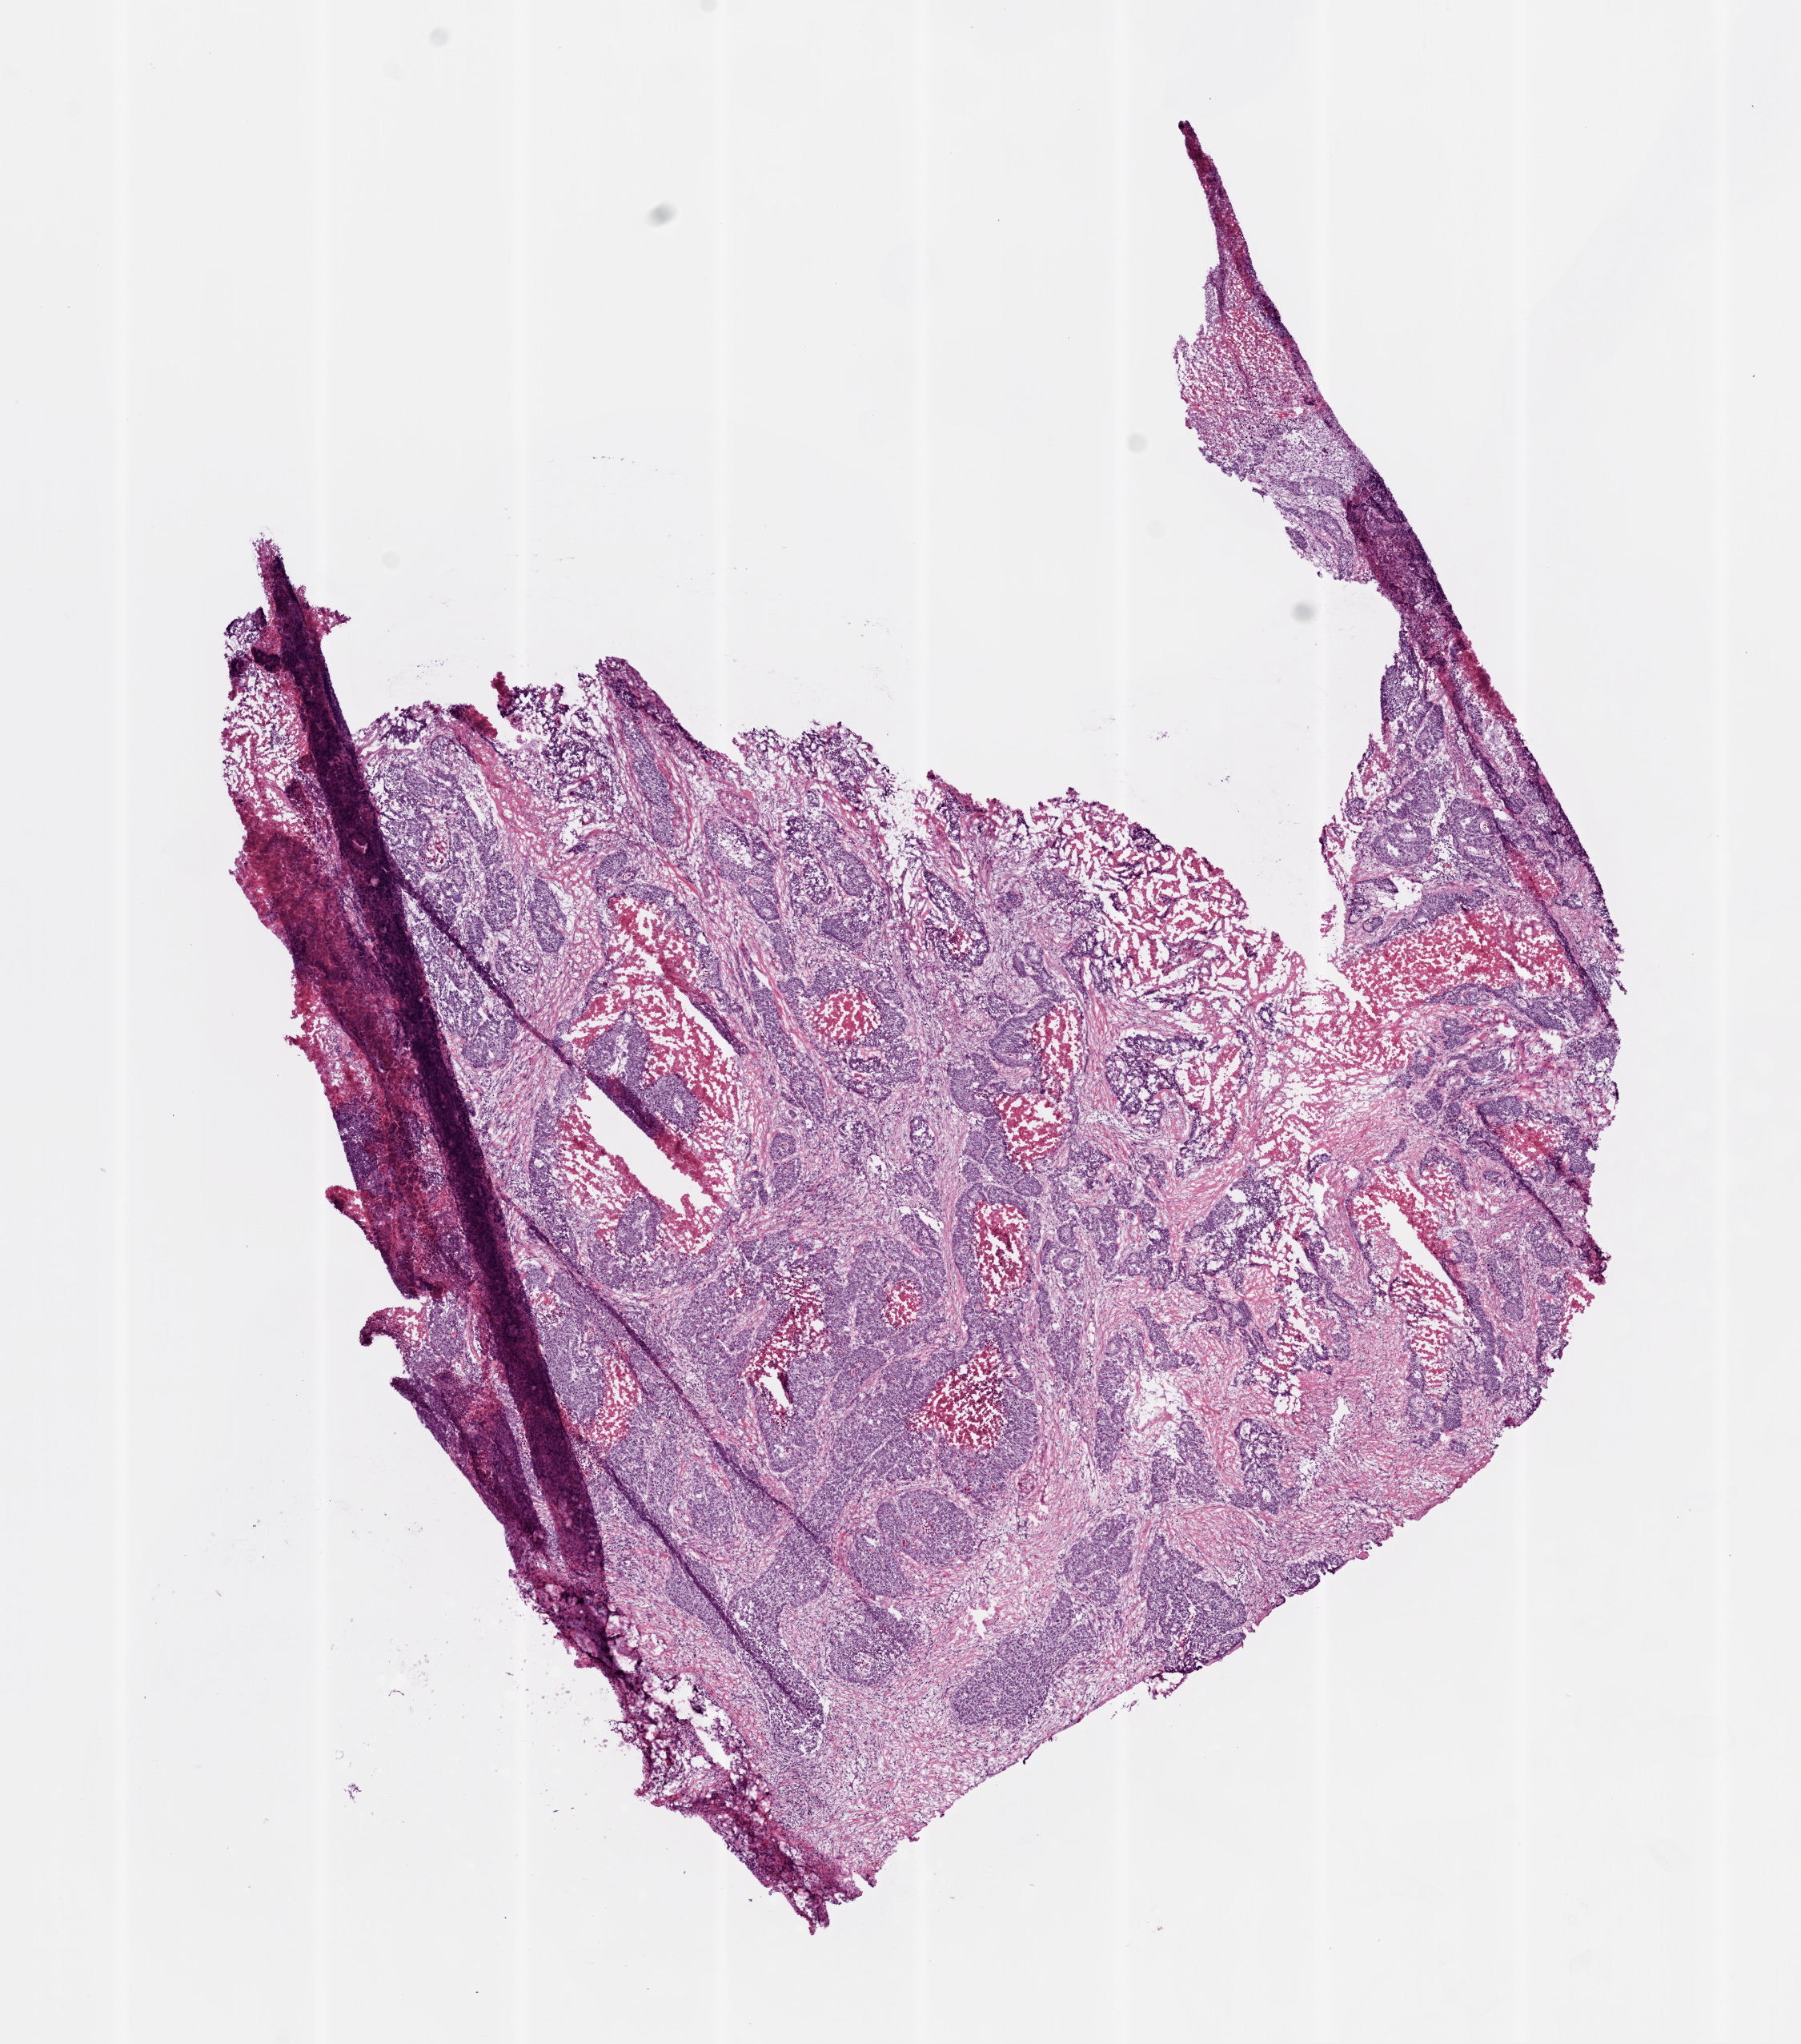
Digitized H&E tissue section (whole slide) — low-resolution overview of the scanned area, about 9.0 x 10.2 mm; frozen section; stomach, primary tumour sample. Patient: male, age at initial diagnosis 66 years. Histologic grade: G3 (poorly differentiated). Slide review estimates, as recorded: tumour cells 62%, tumour nuclei 80%, normal cells 0%, stromal cells 20%, necrosis 18%.
Pathologic diagnosis: Adenocarcinoma, intestinal type (body of stomach). Lymph nodes positive (case pathology): 0 of 22 examined. AJCC pathologic stage: II. TNM: T3 N0 M0.